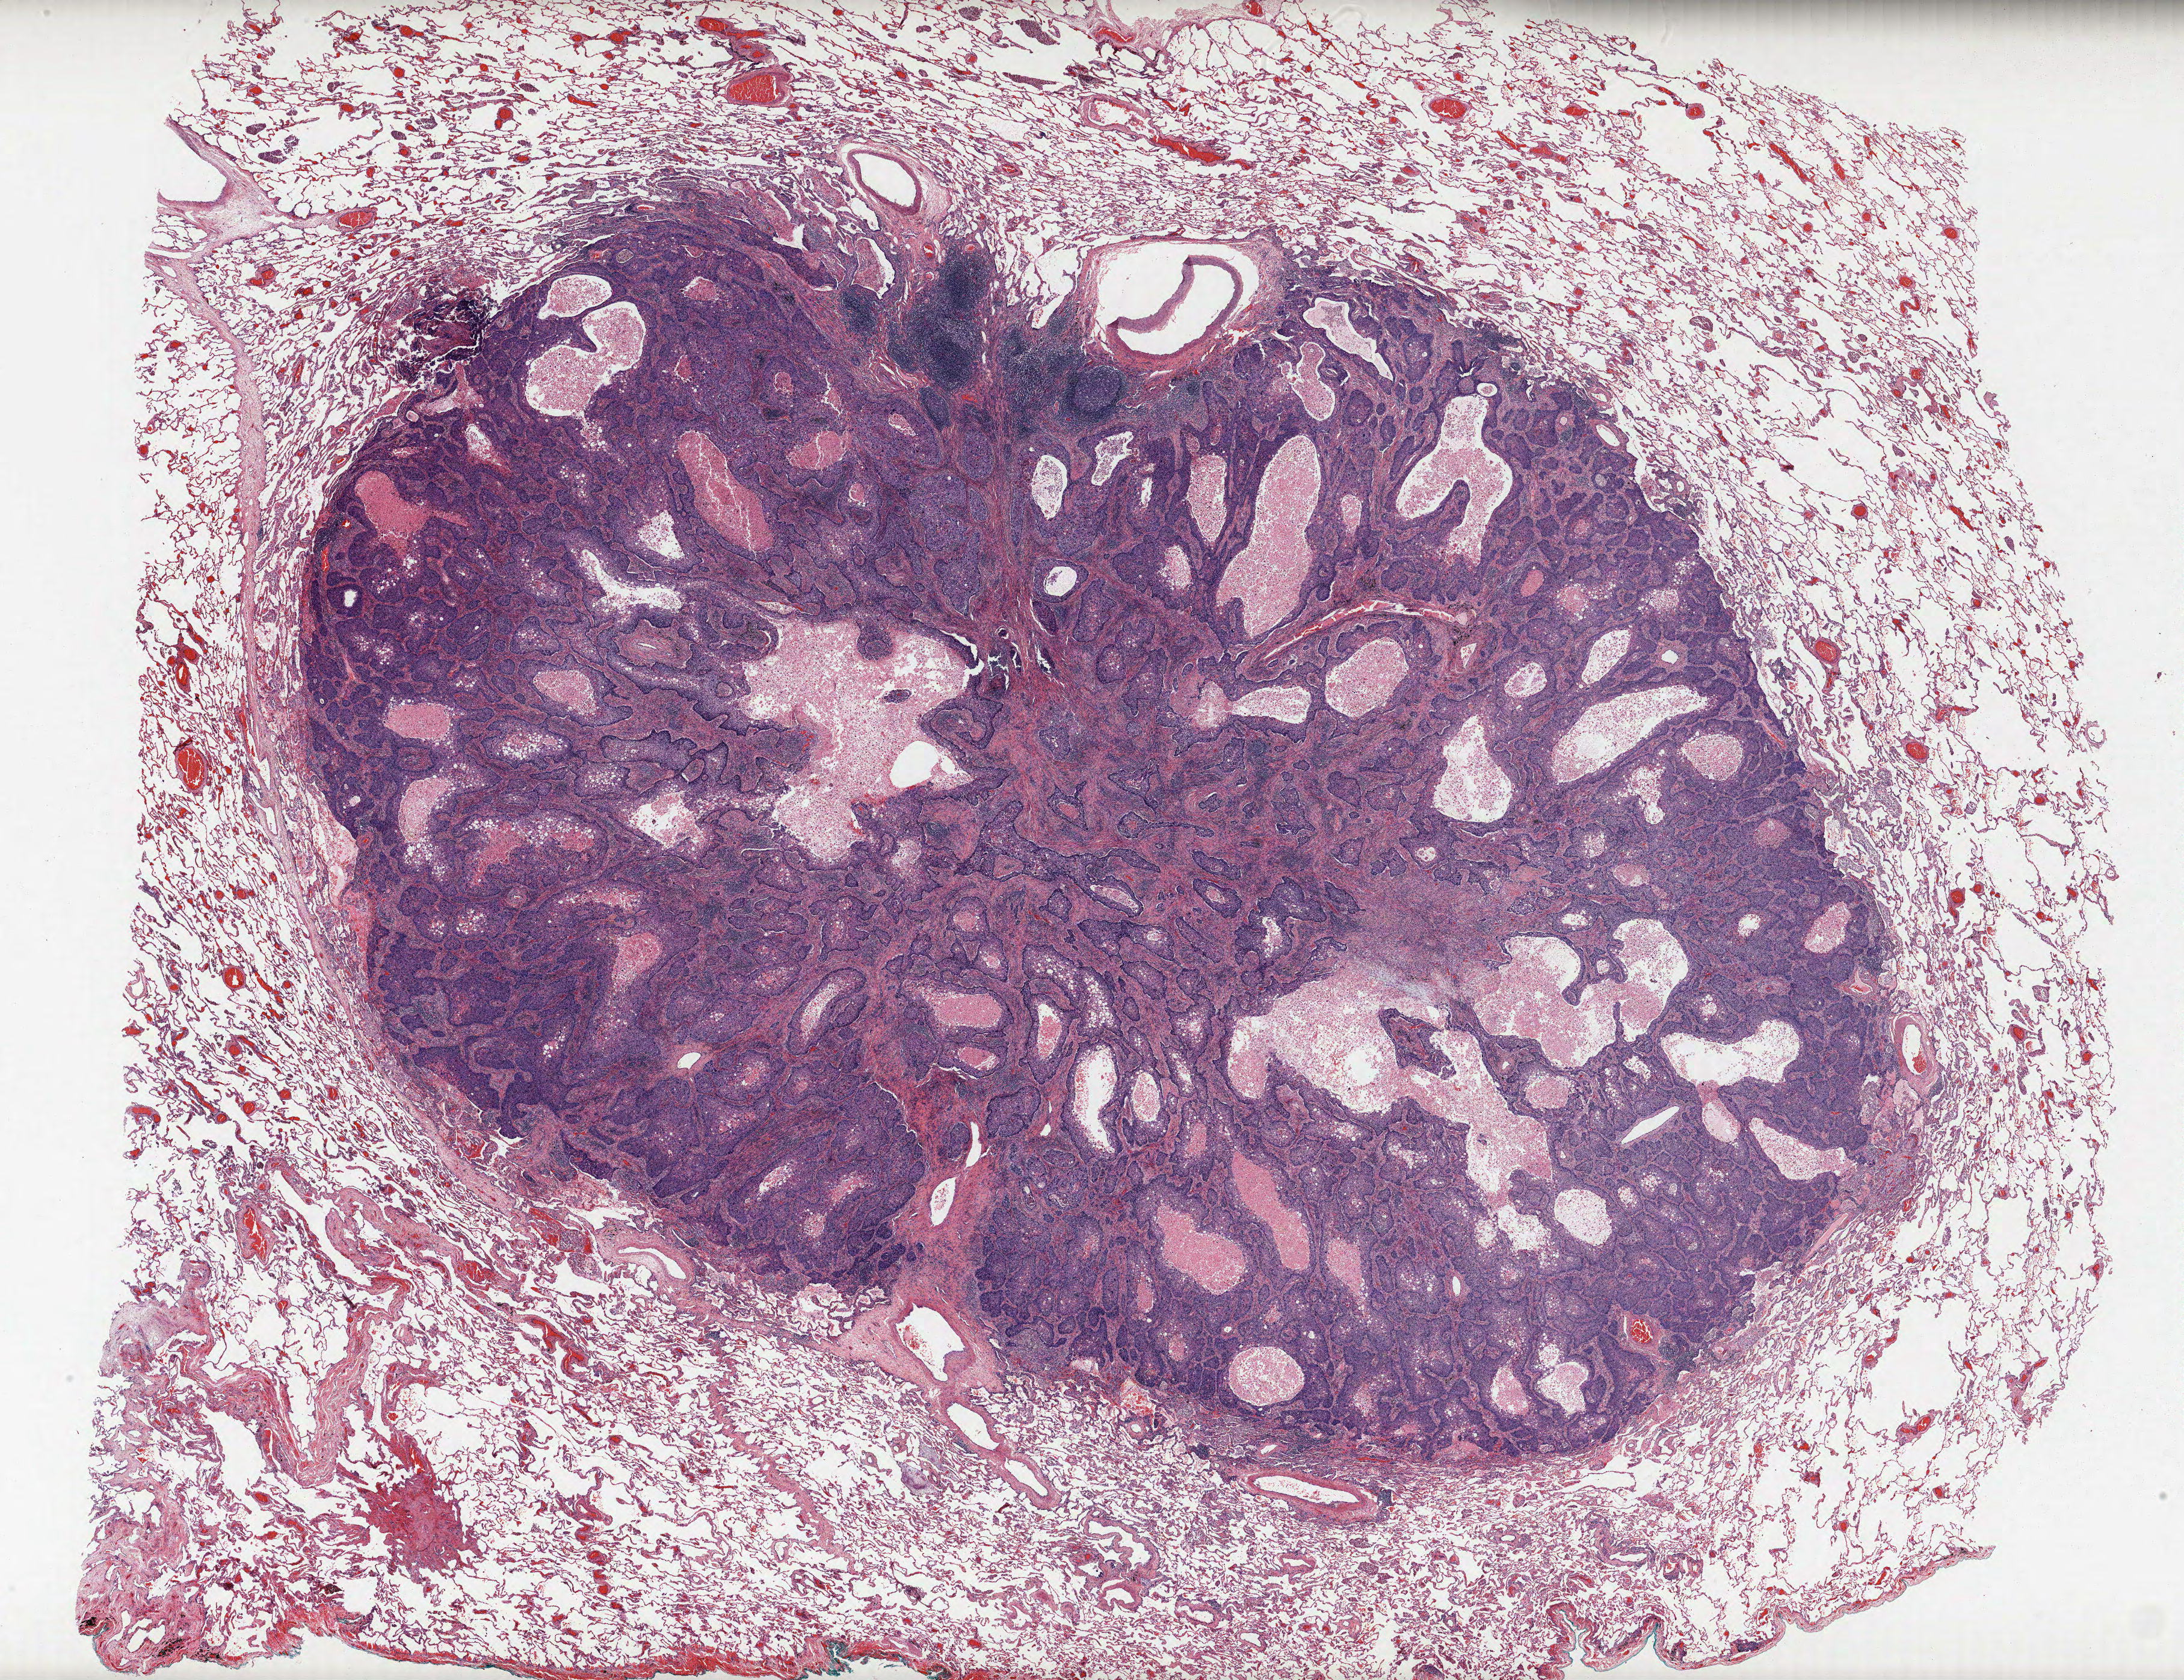
H&E whole-slide image, a low-resolution overview of the entire scanned area, about 29.0 x 22.3 mm (acquisition: 40x scan); formalin-fixed paraffin-embedded (FFPE) section; lung. Male, age 65 at enrolment. Current smoker at enrolment. Grade: moderately differentiated (G2).
- stage (AJCC 6th edition): IA
- primary tumour location (clinical record): left upper lobe
- tumour size (pathology): 25 mm
- participant's lung-cancer diagnosis: Squamous cell carcinoma, NOS (ICD-O-3 8070/3)